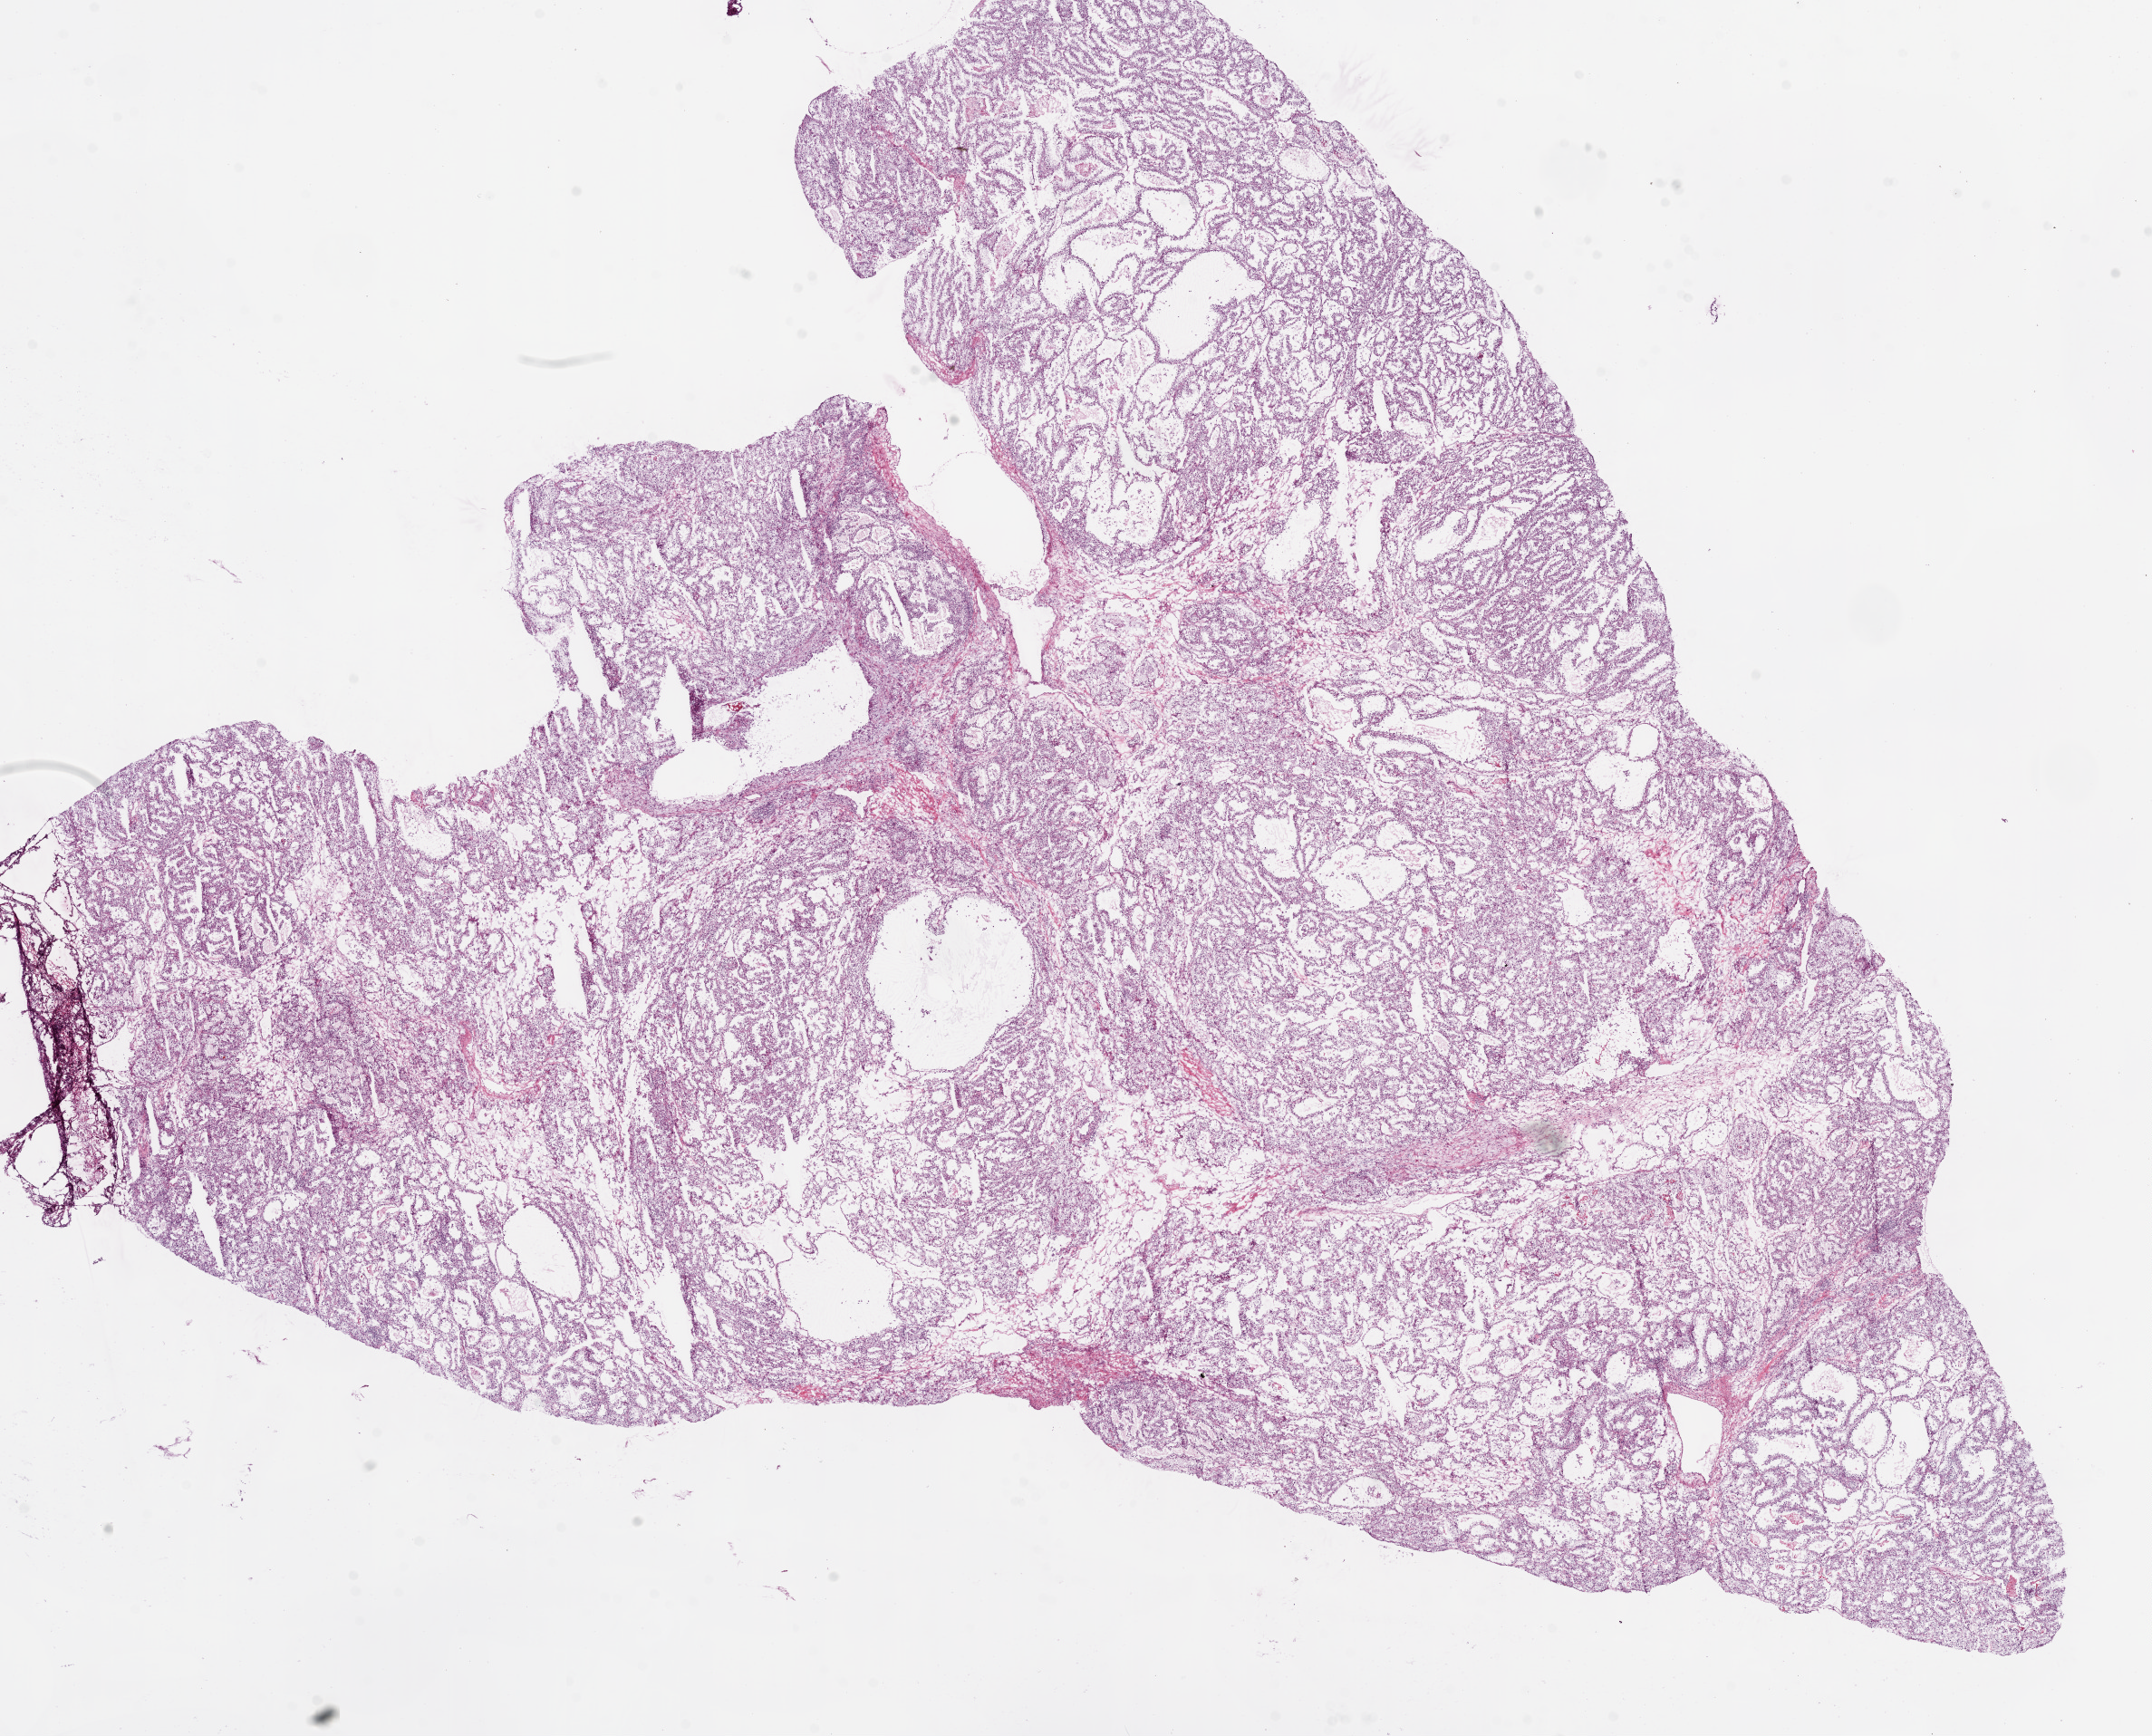
Hematoxylin and eosin (H&E) stained whole-slide image, shown as a low-resolution overview of the whole scanned area (about 19.1 x 15.4 mm, acquisition: 20x scan). Frozen section. Primary tumour sample from the kidney. Patient: female, age at initial diagnosis 70 years. Histologic grade: G2 (moderately differentiated). Composition of this section per pathologist review: tumour cells 90%, tumour nuclei 80%, normal cells 0%, stromal cells 10%, necrosis 0%.
Histologic diagnosis: Clear cell adenocarcinoma, NOS. Laterality: left. AJCC pathologic stage: I. TNM: T1a NX M0.